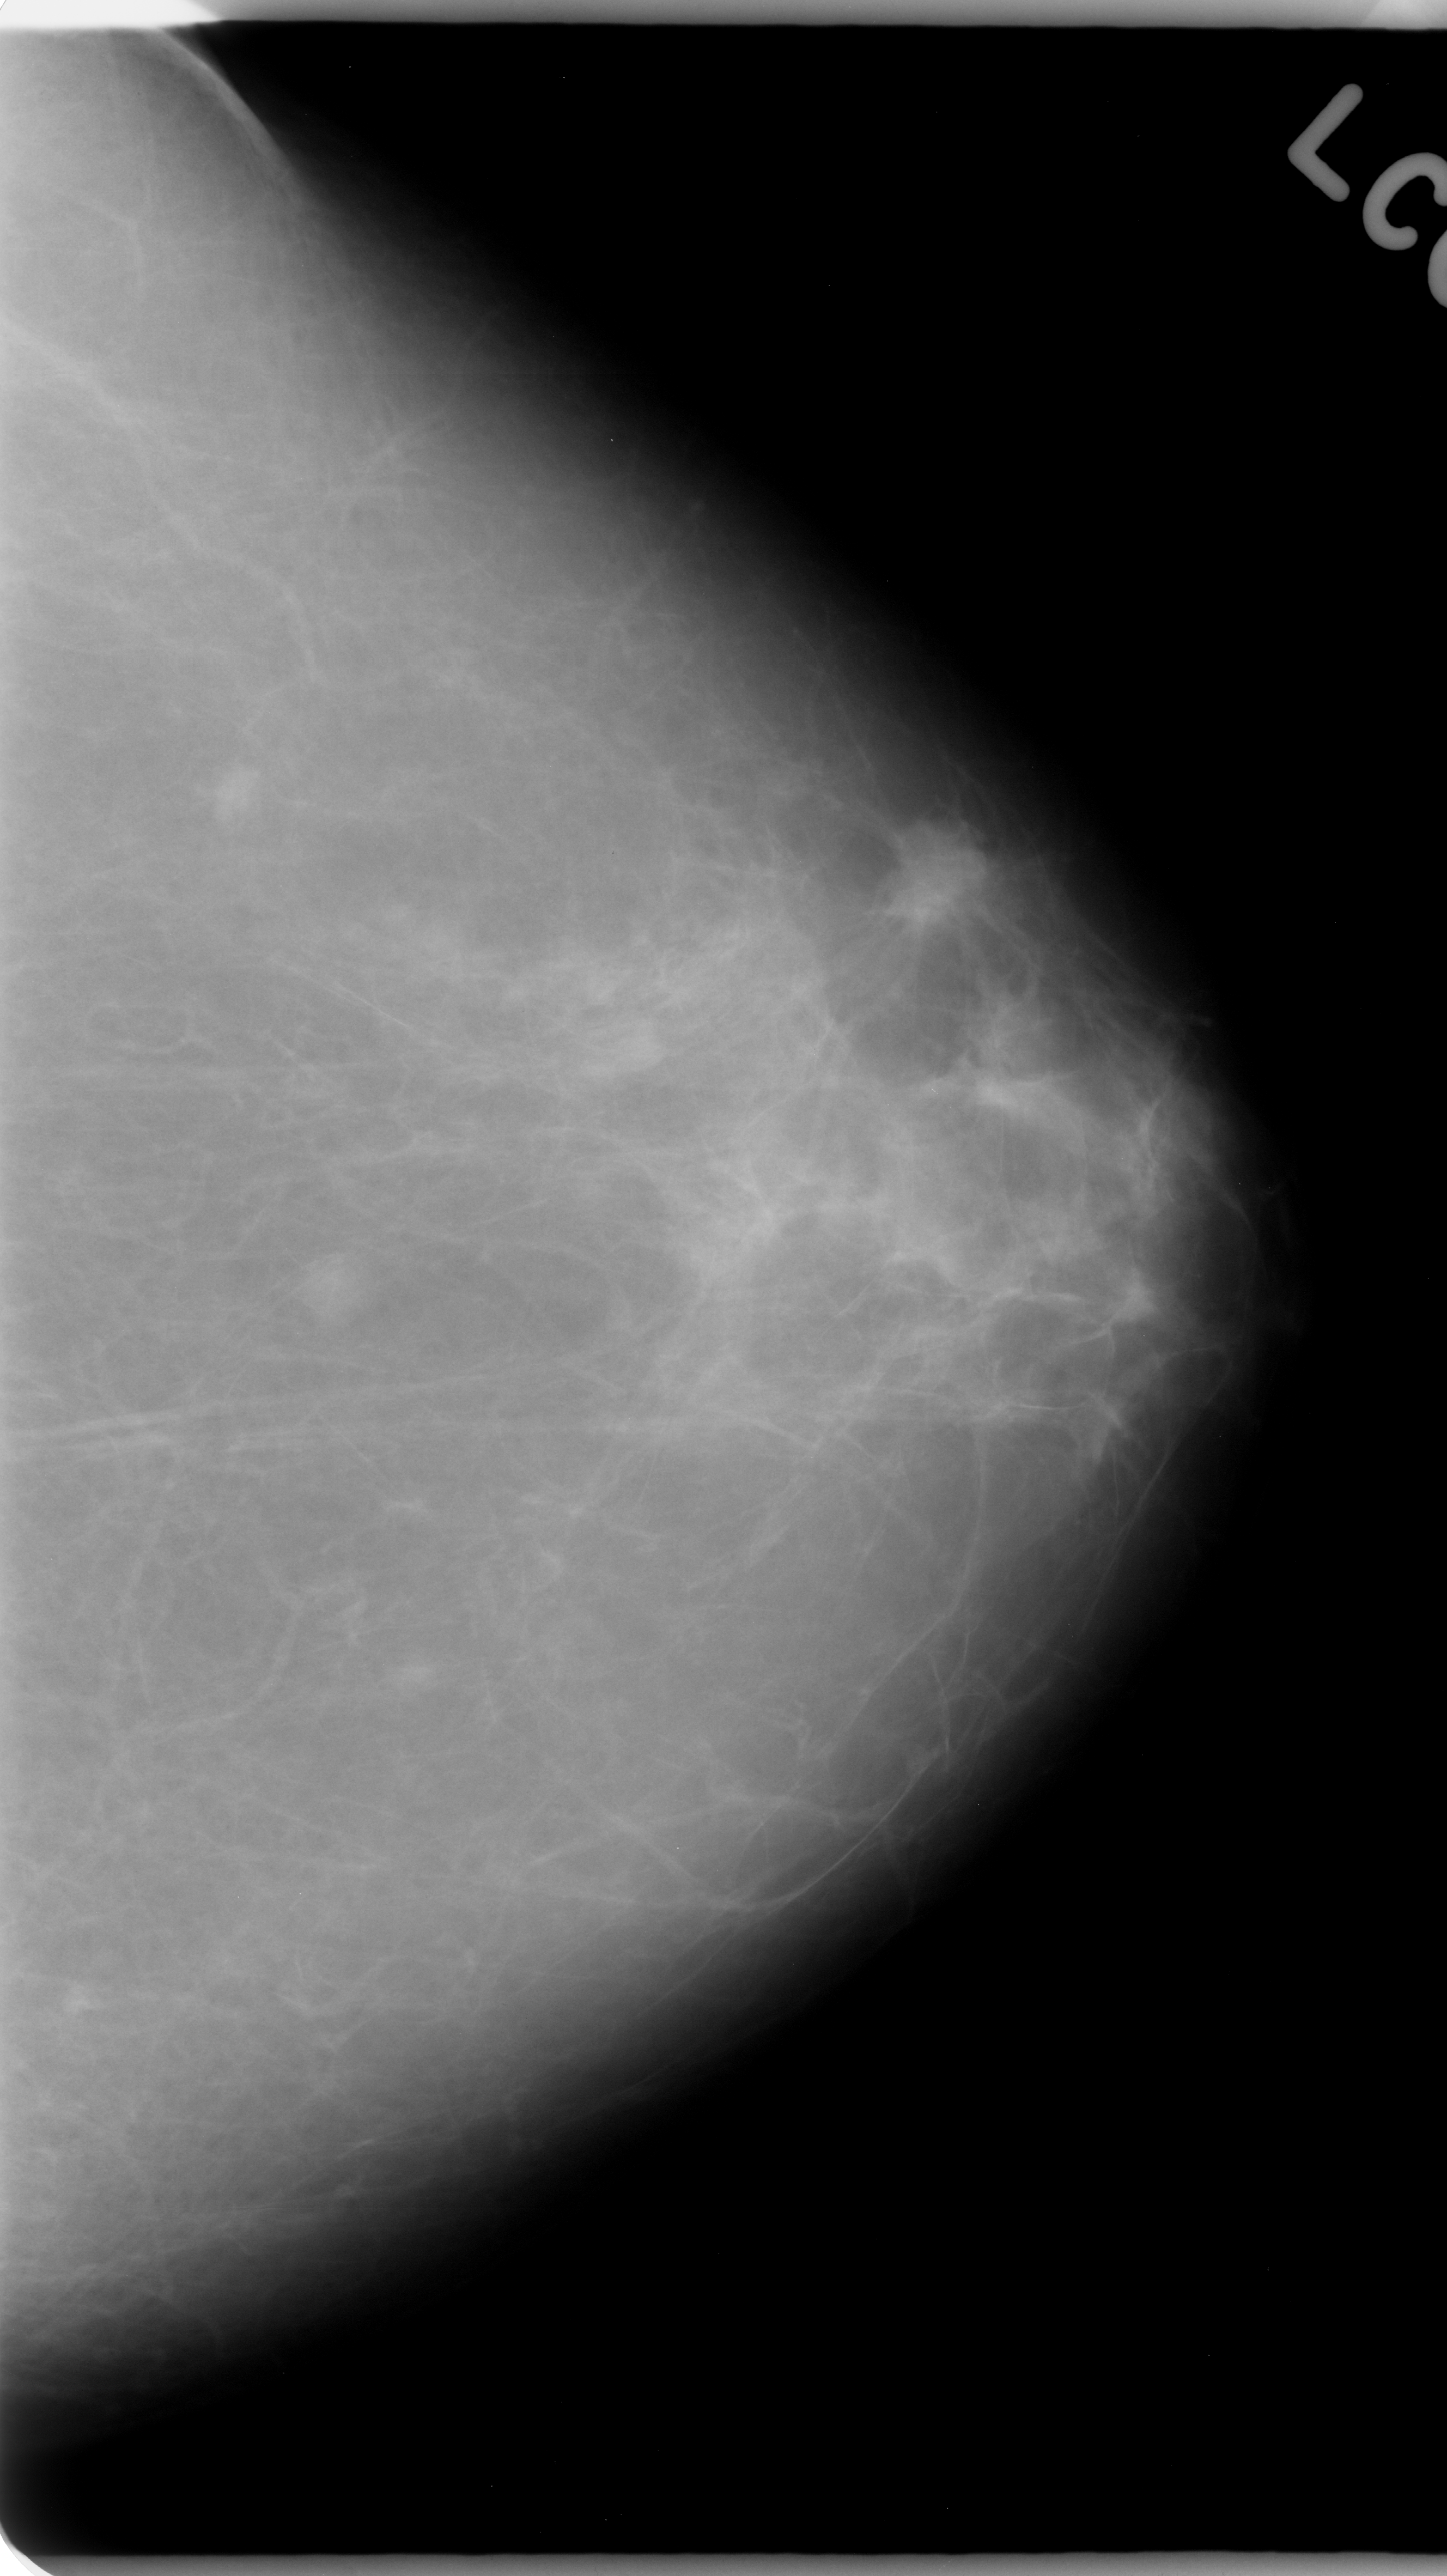
Mammogram (digitized film). Left breast. Craniocaudal (CC) view. BI-RADS breast density category 1 (scale 1–4). 1447 × 2576 image matrix.
Expert-marked regions of interest on this film, with their recorded descriptors:
- mass, shape irregular, margins spiculated; BI-RADS assessment category 5; pathology result (as recorded, not read from the image): malignant: bounding box <535,912,727,1092> (left, top, right, bottom; pixels)